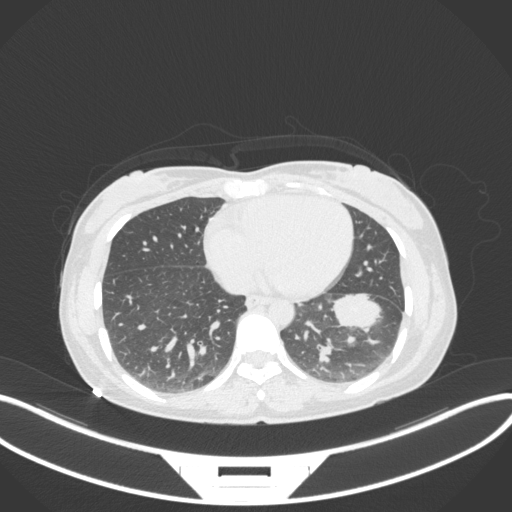
Chest CT, one axial slice; position 129 of 361 along the scan axis; reconstruction kernel B31f; lung window (W 1500 / L -600 HU); 1 mm slice thickness; 512 × 512 image matrix. Patient: female, 41 years. Case-level facts recorded for this patient, not image findings: clinical TNM (as recorded): T2a N3 M1b.
Annotated regions visible in this slice (rectangle marked by the reading radiologist):
- lung tumour (recorded histology: adenocarcinoma): bounding box (x1, y1, x2, y2) in pixels: (333, 291, 384, 331)